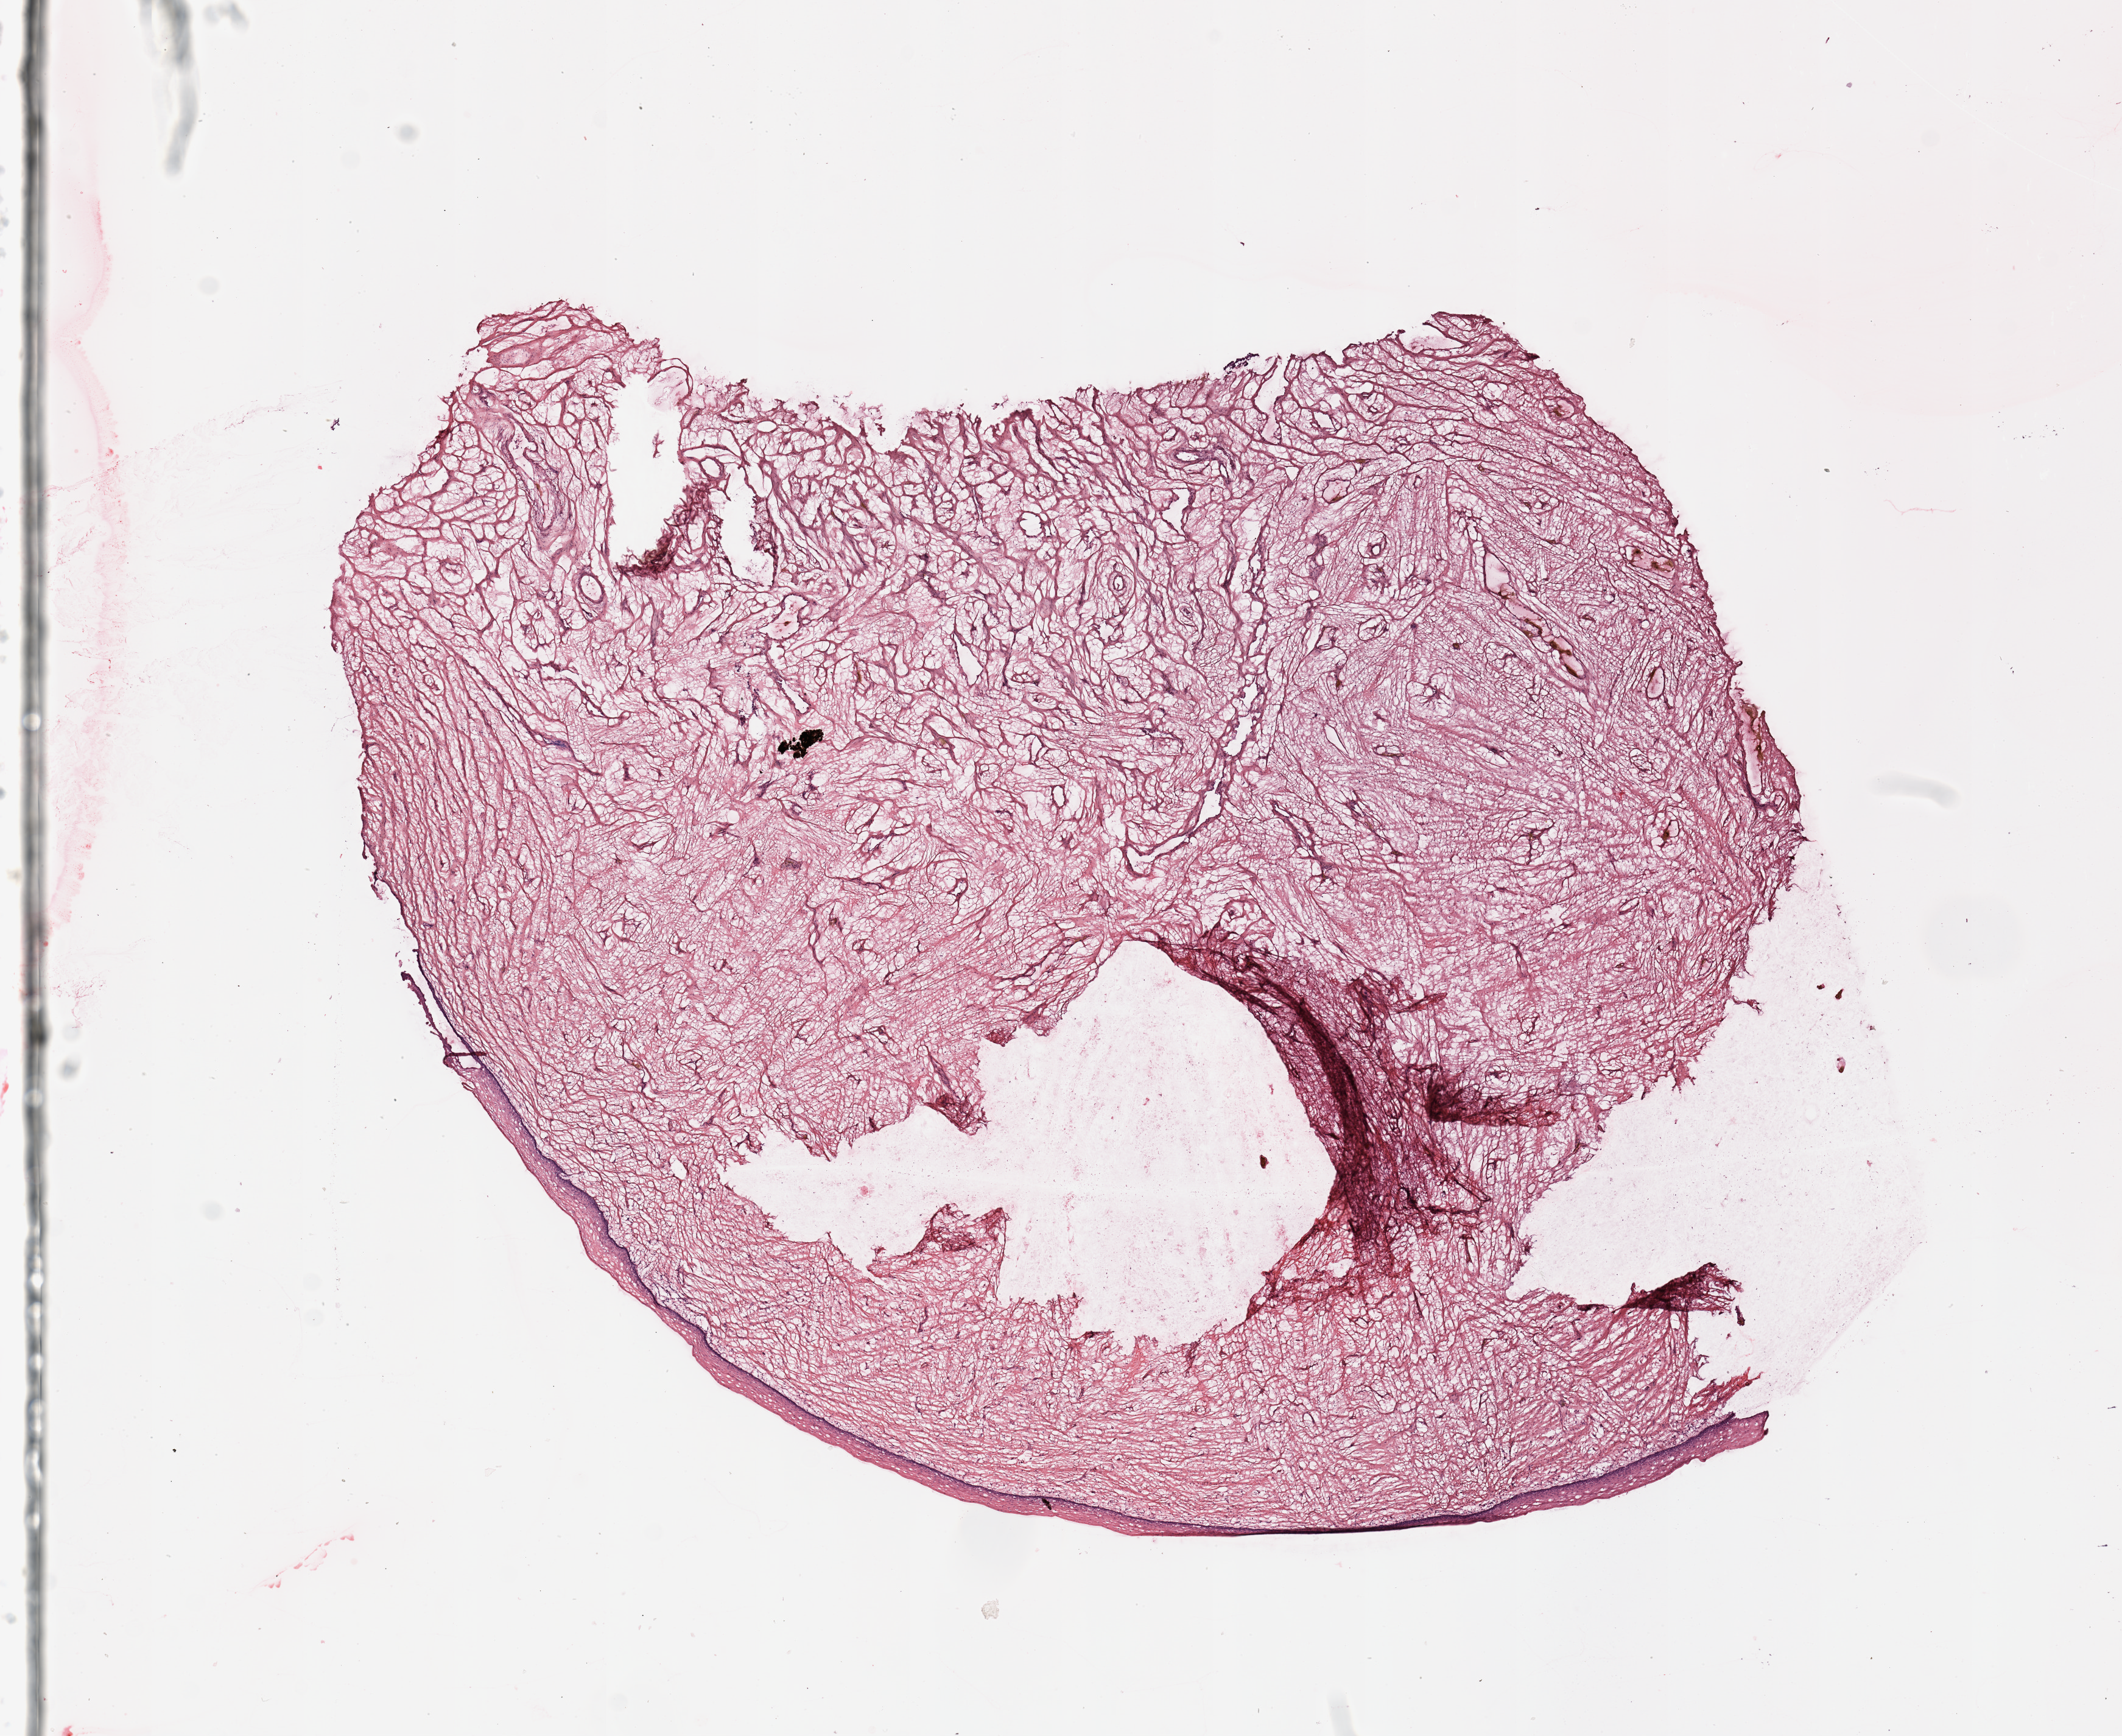
H&E whole-slide image, shown as a low-resolution overview of the whole scanned area (about 13.8 x 11.3 mm, from a 20x scan). Normal (non-tumour) tissue sample, uterus. 44-year-old female patient.
This section: normal (non-tumour) tissue from the same patient. Patient diagnosis: Endometrioid adenocarcinoma, NOS.